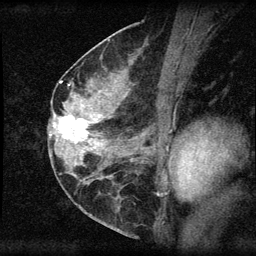
Breast MRI (dynamic contrast-enhanced), one sagittal slice; slice 31 of 60 in the series (ordered by position); dynamic contrast-enhanced series, image 2 of 3 at this slice position (ordered by acquisition); 1.5 T; TE 4.2 ms, TR 8.2 ms; 2 mm slice thickness; 256 × 256 image matrix, field of view 180 × 180 mm. Patient: female, 45 years.
Outlined on this slice (semi-automatically segmented with operator editing):
- analysis volume of interest (the breast-tissue region the enhancement analysis was run in; not a lesion): bounding box <55,110,94,148> (left, top, right, bottom; pixels)
- tumour enhancement mask (voxels above the 70 % enhancement threshold inside the analysis volume of interest): <58,116,87,143>